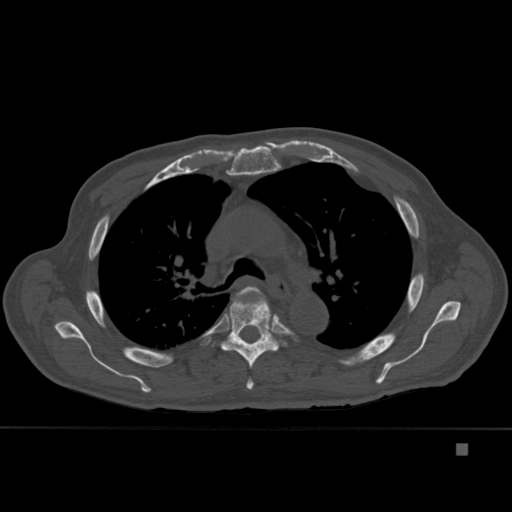
CT including the spine, one axial slice; slice 309 of 451 in the series (ordered by position); bone window (W 1800 / L 400 HU); 512 × 512 image matrix, field of view 378 × 378 mm. Patient: male, 75 years. Case-level facts recorded for this patient, not image findings: primary cancer: prostate.
Structures marked on this image (semi-automatically segmented with operator editing):
- T4 vertebra: bounding box <229,286,266,390> (left, top, right, bottom; pixels)
- T5 vertebra: <220,287,287,369>